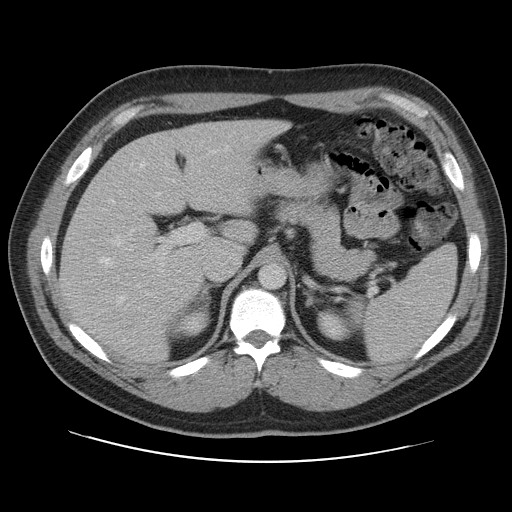
Contrast-enhanced abdominal CT, one axial slice; slice 73 of 109 in the series (ordered by position); 120 kVp; intravenous contrast given; soft-tissue window (W 400 / L 40 HU); 5 mm slice thickness; 512 × 512 image matrix. Male patient, age 35 years. Case-level facts recorded for this patient, not image findings: diagnosis: colorectal cancer liver metastases, imaged before liver resection; multiple liver metastases: yes; largest metastasis: 2.8 cm; disease in both lobes: yes.
Annotated regions visible in this slice (expert manual segmentation):
- hepatic veins: bounding box <99,146,229,304> (left, top, right, bottom; pixels)
- liver: <61,120,285,361>
- planned liver remnant (the part of the liver to remain after resection): <61,120,281,360>
- portal vein (with intrahepatic branches): <117,160,207,298>